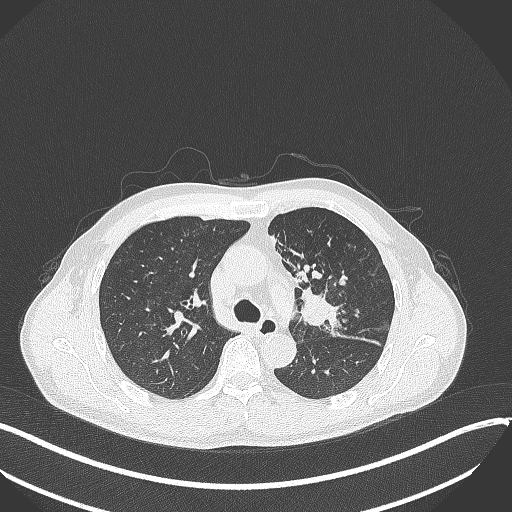
Chest CT, one axial slice. Slice 229 of 411 in the series (ordered by position). 120 kVp. Lung window (W 1500 / L -600 HU). 1 mm slice thickness. 512 × 512 image matrix, field of view 400 × 400 mm. Male patient, age 56 years. Case-level facts recorded for this patient, not image findings: clinical TNM (as recorded): T2a N0 M0.
Structures marked on this image (rectangle marked by the reading radiologist):
- lung tumour (recorded histology: squamous cell carcinoma): box from (x=294, y=282) to (x=349, y=332) px